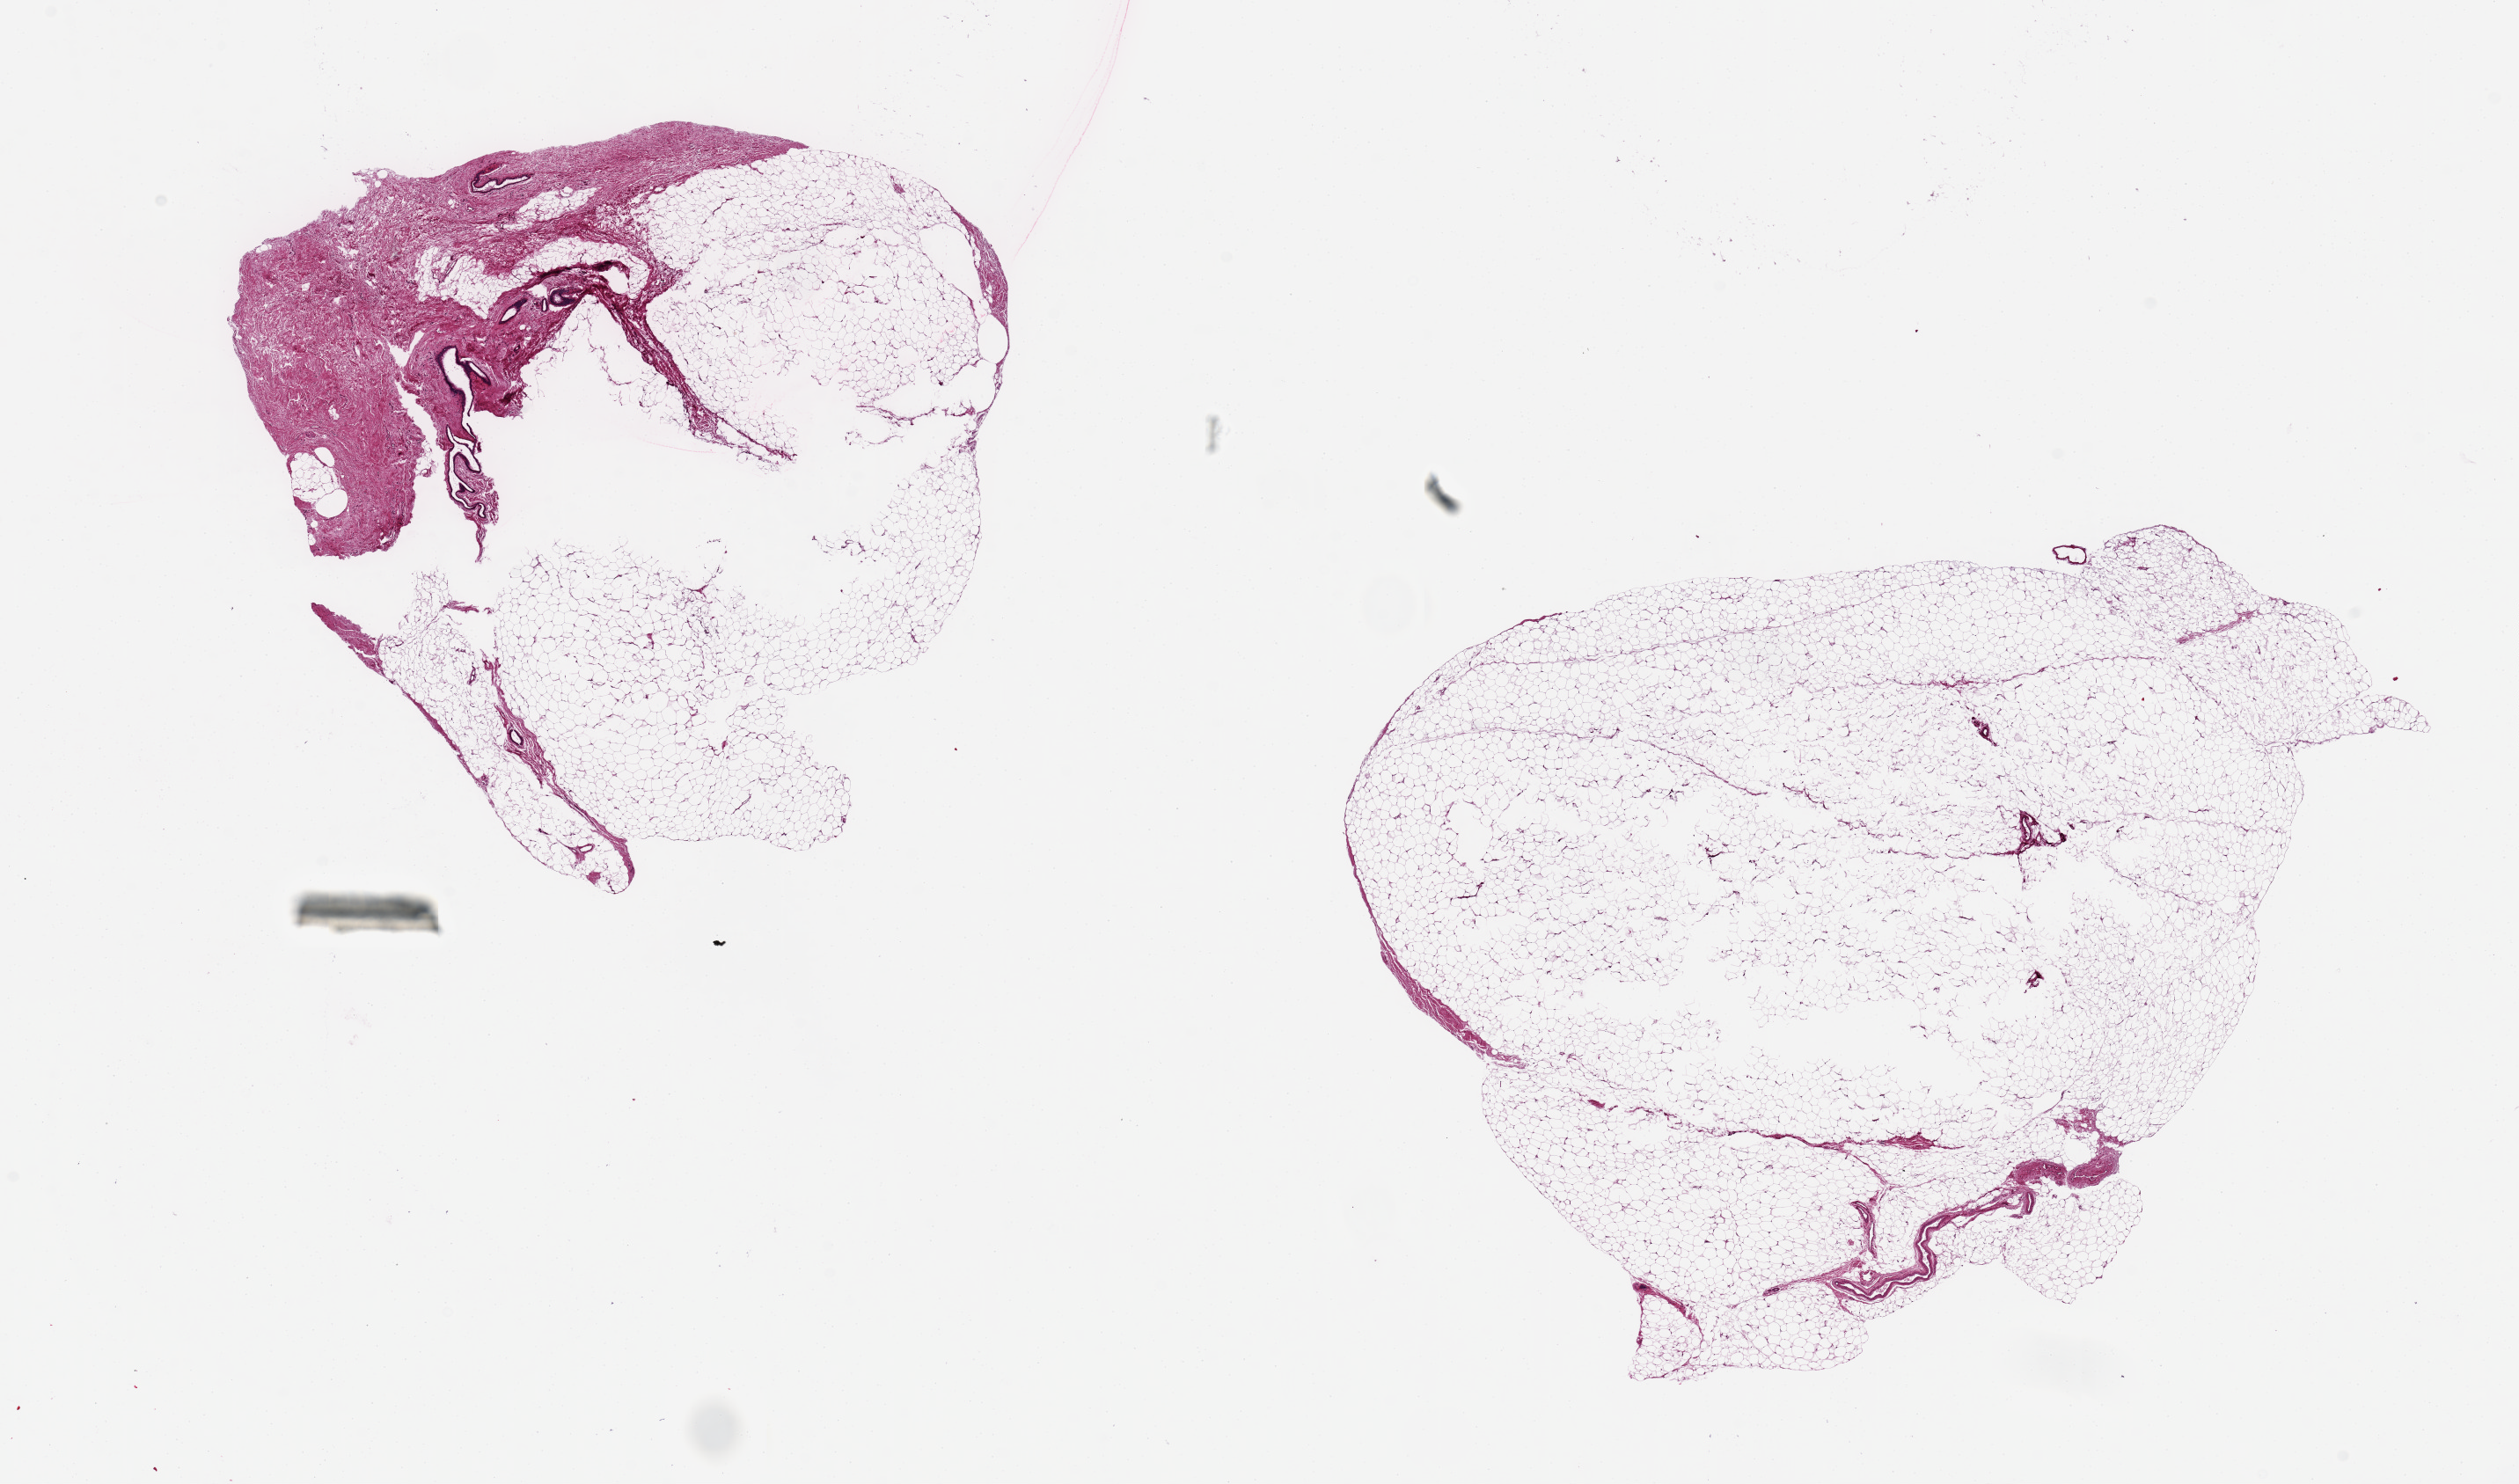
Digitized hematoxylin and eosin (H&E)-stained section — whole scanned area (about 22.6 x 13.3 mm, slide scanned at 20x) shown as a low-resolution overview; PAXgene-fixed paraffin-embedded (PFPE) section; section of breast (target tissue); donor tissue sample. Donor: male.
- review note (as recorded): 2 aliquots. One all adipose tissue, the other with focal ductal elements